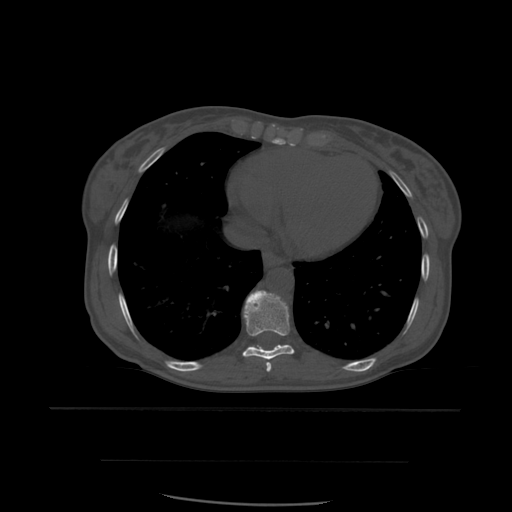
CT including the spine, one axial slice. Bone window (W 1800 / L 400 HU). 1.25 mm slice thickness. 512 × 512 image matrix, field of view 392 × 392 mm. Patient age 48 years. Case-level facts recorded for this patient, not image findings: primary cancer: lung; vertebrae with lytic lesions (as recorded): T11.
Outlined on this slice (semi-automatic segmentation, software-assisted and operator-edited):
- T8 vertebra: bounding box [x1, y1, x2, y2] px = [266, 362, 272, 372]
- T9 vertebra: [242, 290, 295, 360]